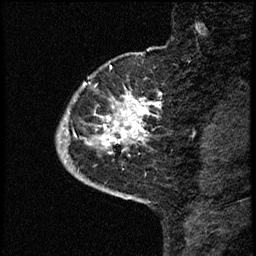
Breast MRI (dynamic contrast-enhanced), one sagittal slice. Slice 11 of 68 in the series (ordered by position). Dynamic contrast-enhanced study with each time point stored as its own series, time point 2 of 3 at this slice position (early post-contrast, ordered by acquisition time). 1.5 T. TE 4.2 ms, TR 17.6 ms. 2 mm slice thickness. 256 × 256 image matrix. Patient: female, 52 years. Case-level facts recorded for this patient, not image findings: setting: breast cancer imaged before/during neoadjuvant chemotherapy; receptor status: HER2-positive.
Outlined on this slice (semi-automatically segmented with operator editing):
- analysis volume of interest (the breast-tissue region the enhancement analysis was run in; not a lesion): bounding box <58,61,166,184> (left, top, right, bottom; pixels)
- tumour enhancement mask (voxels above the 100 % enhancement threshold inside the analysis volume of interest): <63,95,160,153>